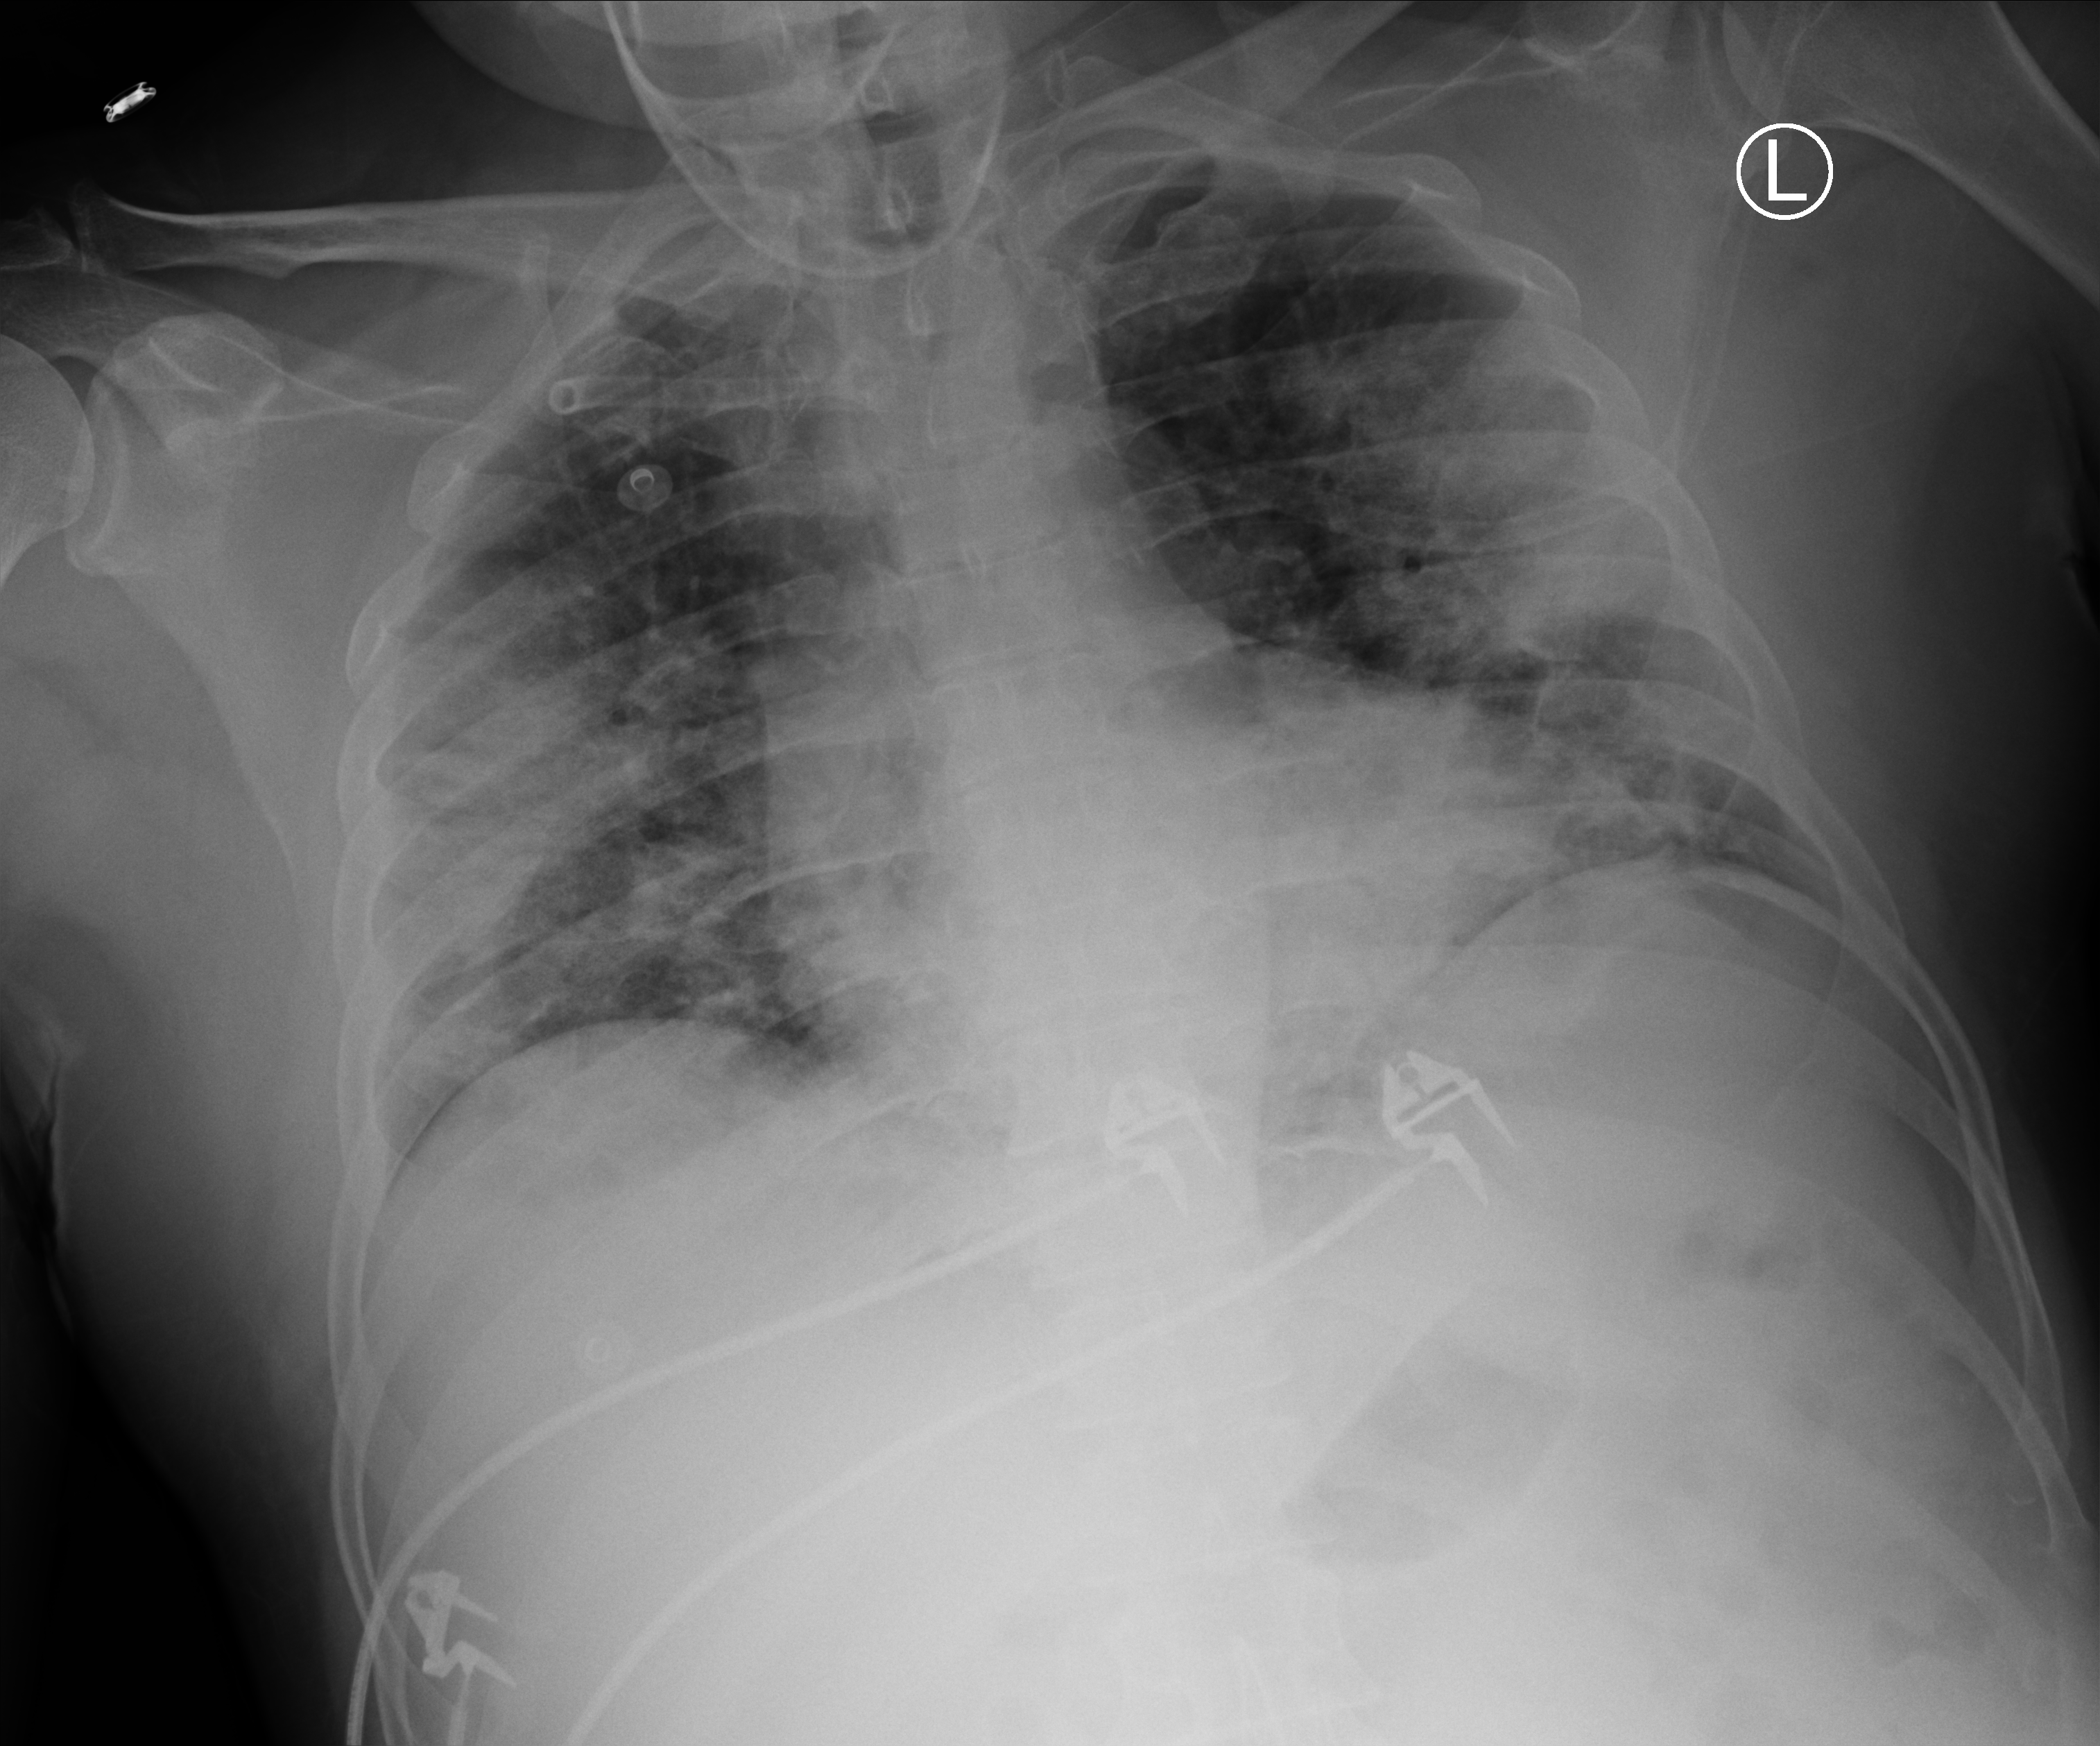
Portable chest radiograph; anteroposterior (AP) projection. Male patient hospitalised with COVID-19, age 18–59 years.
Admission-level facts for this patient (not findings on this image; timing relative to this image not recorded): mechanically ventilated during this hospital stay: yes; admitted to intensive care during this hospital stay: yes; hypertension (admission record): no.